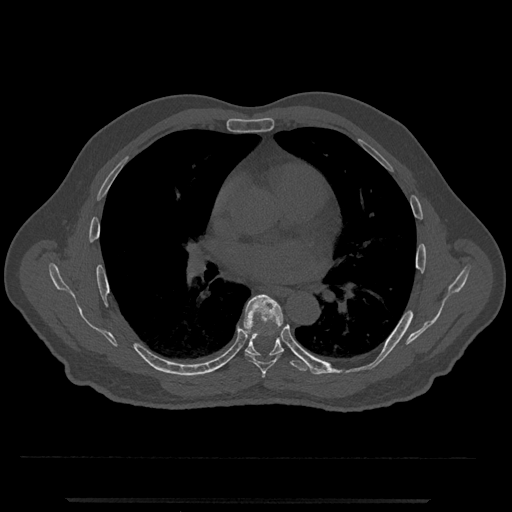
CT including the spine, one axial slice. Reconstruction kernel Br40s/3. 120 kVp. Bone window (W 1800 / L 400 HU). 512 × 512 image matrix, field of view 419 × 419 mm. Patient: male, 63 years. From the clinical record (not read from this slice): primary cancer: prostate.
Outlined on this slice (semi-automatically segmented with operator editing):
- T5 vertebra: box from (x=262, y=373) to (x=265, y=378) px
- T6 vertebra: (x=244, y=294)–(x=283, y=374)
- T7 vertebra: (x=224, y=294)–(x=324, y=375)